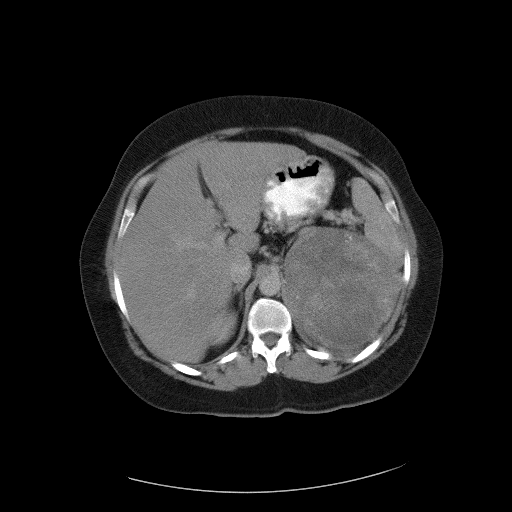
Contrast-enhanced abdominal CT, one axial slice. Slice 72 of 90 in the series (ordered by position). 120 kVp. Intravenous contrast given. Soft-tissue window (W 400 / L 40 HU). 5 mm slice thickness. 512 × 512 image matrix. Patient: female, 55 years. Case-level facts recorded for this patient, not image findings: diagnosis: adrenocortical carcinoma; tumour side: left adrenal; tumour size at pathology: 22 cm; Ki-67 index: 10 %.
Annotated regions visible in this slice (semi-automatically segmented with operator editing):
- mass: bounding box [x1, y1, x2, y2] px = [284, 227, 397, 346]